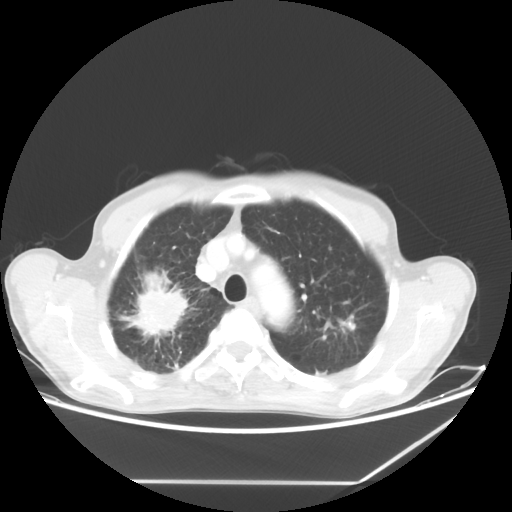
Chest CT, one axial slice; slice 50 of 65 in the series (ordered by position); 80 kVp; lung window (W 1500 / L -600 HU); 5 mm slice thickness; 512 × 512 image matrix, field of view 397 × 397 mm. Male patient, age 68 years. Case-level facts recorded for this patient, not image findings: clinical TNM (as recorded): T3 N3 M0.
Annotated regions visible in this slice (bounding box drawn by a radiologist):
- lung tumour (recorded histology: adenocarcinoma): box from (x=128, y=265) to (x=198, y=353) px